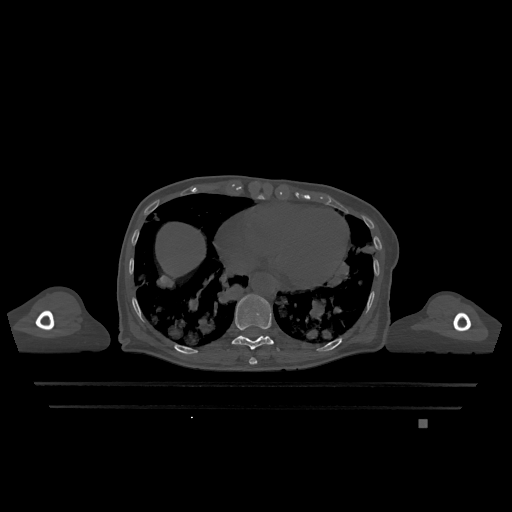
CT including the spine, one axial slice. Slice 640 of 1317 in the series (ordered by position). Bone window (W 1800 / L 400 HU). 512 × 512 image matrix, field of view 500 × 500 mm. Female patient, age 74 years. Case-level facts recorded for this patient, not image findings: primary cancer: lung; vertebrae with lytic lesions (as recorded): T1, T4, T5, T6, L4, L5.
Annotated regions visible in this slice (semi-automatic segmentation, software-assisted and operator-edited):
- T10 vertebra: bounding box (x1, y1, x2, y2) in pixels: (232, 294, 280, 351)
- T9 vertebra: (249, 357, 257, 365)